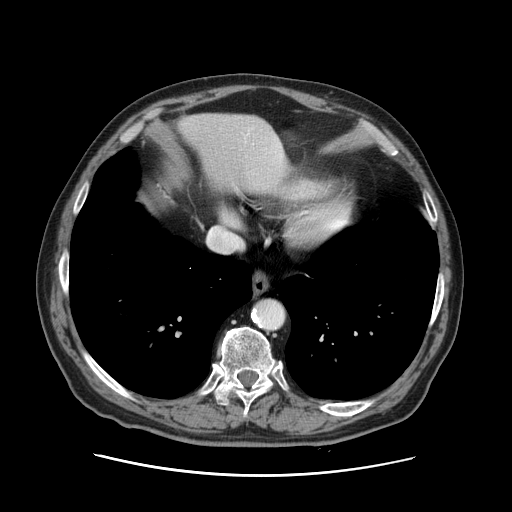
Contrast-enhanced abdominal CT, one axial slice; position 120 of 141 along the scan axis; soft-tissue window (W 400 / L 40 HU); 2.5 mm slice thickness; 512 × 512 image matrix. Male patient, age 72 years. From the clinical record (not read from this slice): diagnosis: colorectal cancer liver metastases, imaged before liver resection; multiple liver metastases: yes; largest metastasis: 5.4 cm; disease in both lobes: yes.
Annotated regions visible in this slice (outlined manually by an expert reader):
- hepatic veins: bounding box [x1, y1, x2, y2] px = [246, 130, 250, 137]
- liver: [179, 114, 286, 193]
- planned liver remnant (the part of the liver to remain after resection): [180, 114, 286, 193]